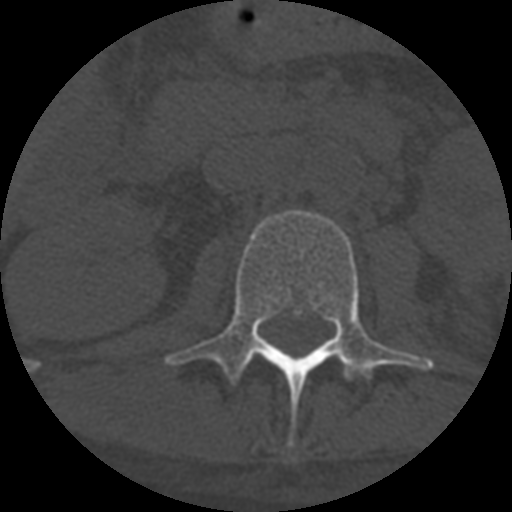
CT including the spine, one axial slice. Slice 264 of 708 in the series (ordered by position). Reconstruction kernel STANDARD. 120 kVp. One of 3 acquisitions stored at this slice position. Bone window (W 1800 / L 400 HU). 1.25 mm slice thickness. 512 × 512 image matrix, field of view 160 × 160 mm. Patient age 55 years. Case-level facts recorded for this patient, not image findings: primary cancer: colon; vertebrae with lytic lesions (as recorded): T12, L1, L5.
Outlined on this slice (semi-automatic segmentation, software-assisted and operator-edited):
- L2 vertebra: box from (x=167, y=210) to (x=434, y=414) px